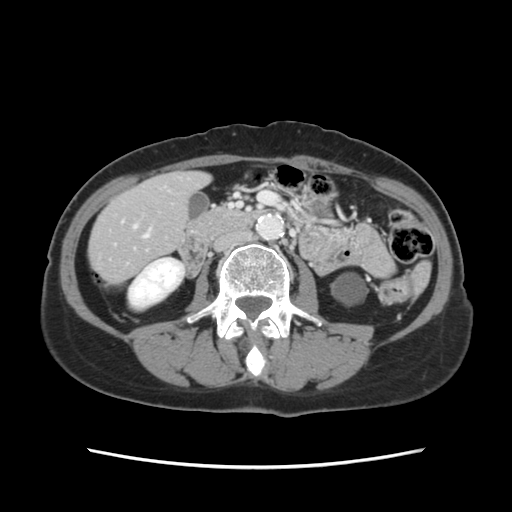
Contrast-enhanced abdominal CT, one axial slice; slice 25 of 120 in the series (ordered by position); 120 kVp; intravenous contrast given; soft-tissue window (W 400 / L 40 HU); 512 × 512 image matrix, field of view 330 × 330 mm. Female patient, age 70 years. From the clinical record (not read from this slice): diagnosis: colorectal cancer liver metastases, imaged before liver resection; multiple liver metastases: no; largest metastasis: 2.5 cm.
Annotated regions visible in this slice (manually delineated by an expert):
- hepatic veins: box from (x=144, y=234) to (x=149, y=238) px
- liver: (x=91, y=173)–(x=206, y=280)
- planned liver remnant (the part of the liver to remain after resection): (x=91, y=173)–(x=206, y=280)
- portal vein (with intrahepatic branches): (x=133, y=225)–(x=138, y=229)